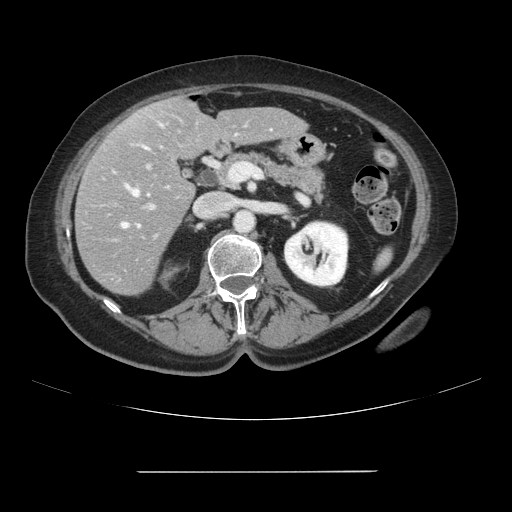
Contrast-enhanced abdominal CT, one axial slice. Position 43 of 111 along the scan axis. 120 kVp. Intravenous contrast given. Soft-tissue window (W 400 / L 40 HU). 2.5 mm slice thickness. 512 × 512 image matrix, field of view 400 × 400 mm. Female patient, age 74 years. From the clinical record (not read from this slice): diagnosis: colorectal cancer liver metastases, imaged before liver resection; multiple liver metastases: yes; largest metastasis: 1.1 cm; chemotherapy before resection: yes.
Outlined on this slice (outlined manually by an expert reader):
- hepatic veins: bounding box [x1, y1, x2, y2] px = [122, 148, 147, 228]
- liver: [75, 97, 306, 296]
- planned liver remnant (the part of the liver to remain after resection): [141, 97, 306, 159]
- portal vein (with intrahepatic branches): [149, 205, 153, 208]